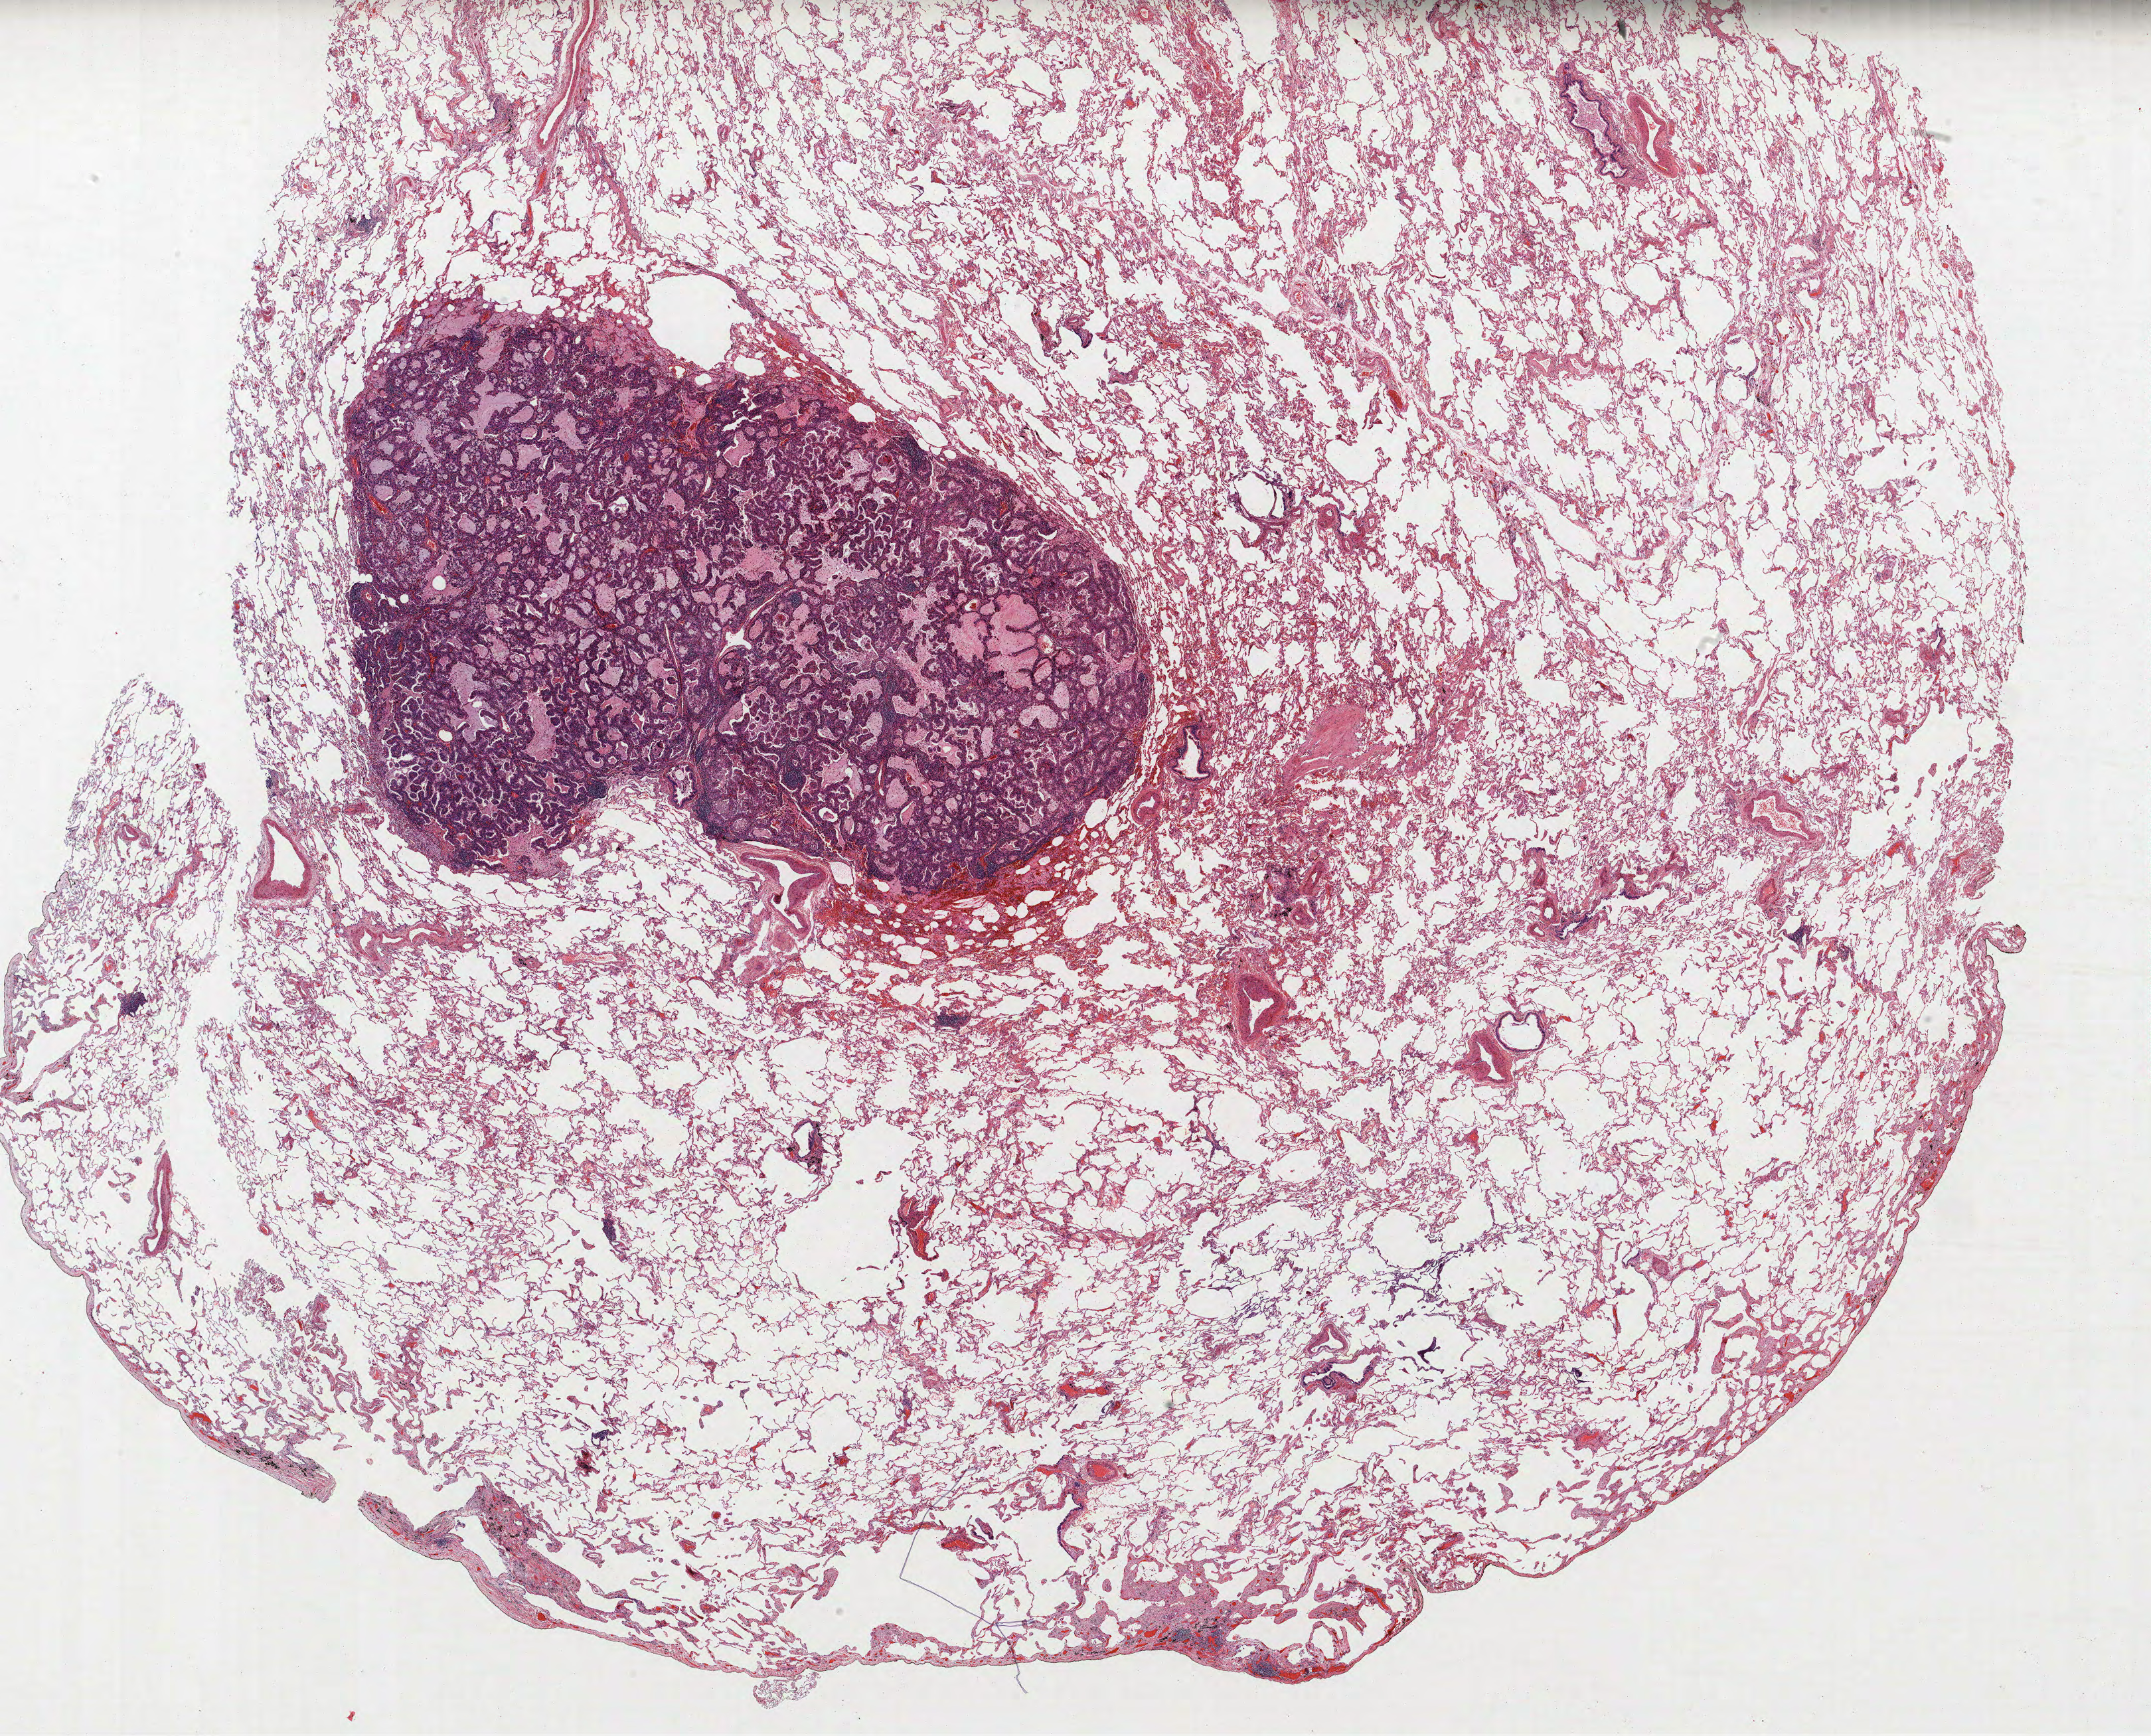
Whole-slide histology image, H&E-stained, low-resolution overview of the scanned area, about 25.9 x 20.9 mm. Formalin-fixed paraffin-embedded (FFPE) section. Lung. Male, age 65 at enrolment. Former smoker at enrolment. Grade: moderately differentiated (G2).
Tumour size (pathology): 11 mm. Stage (AJCC 6th edition): IA. Participant's lung-cancer diagnosis: Adenocarcinoma, NOS. Primary tumour location (clinical record): right upper lobe.